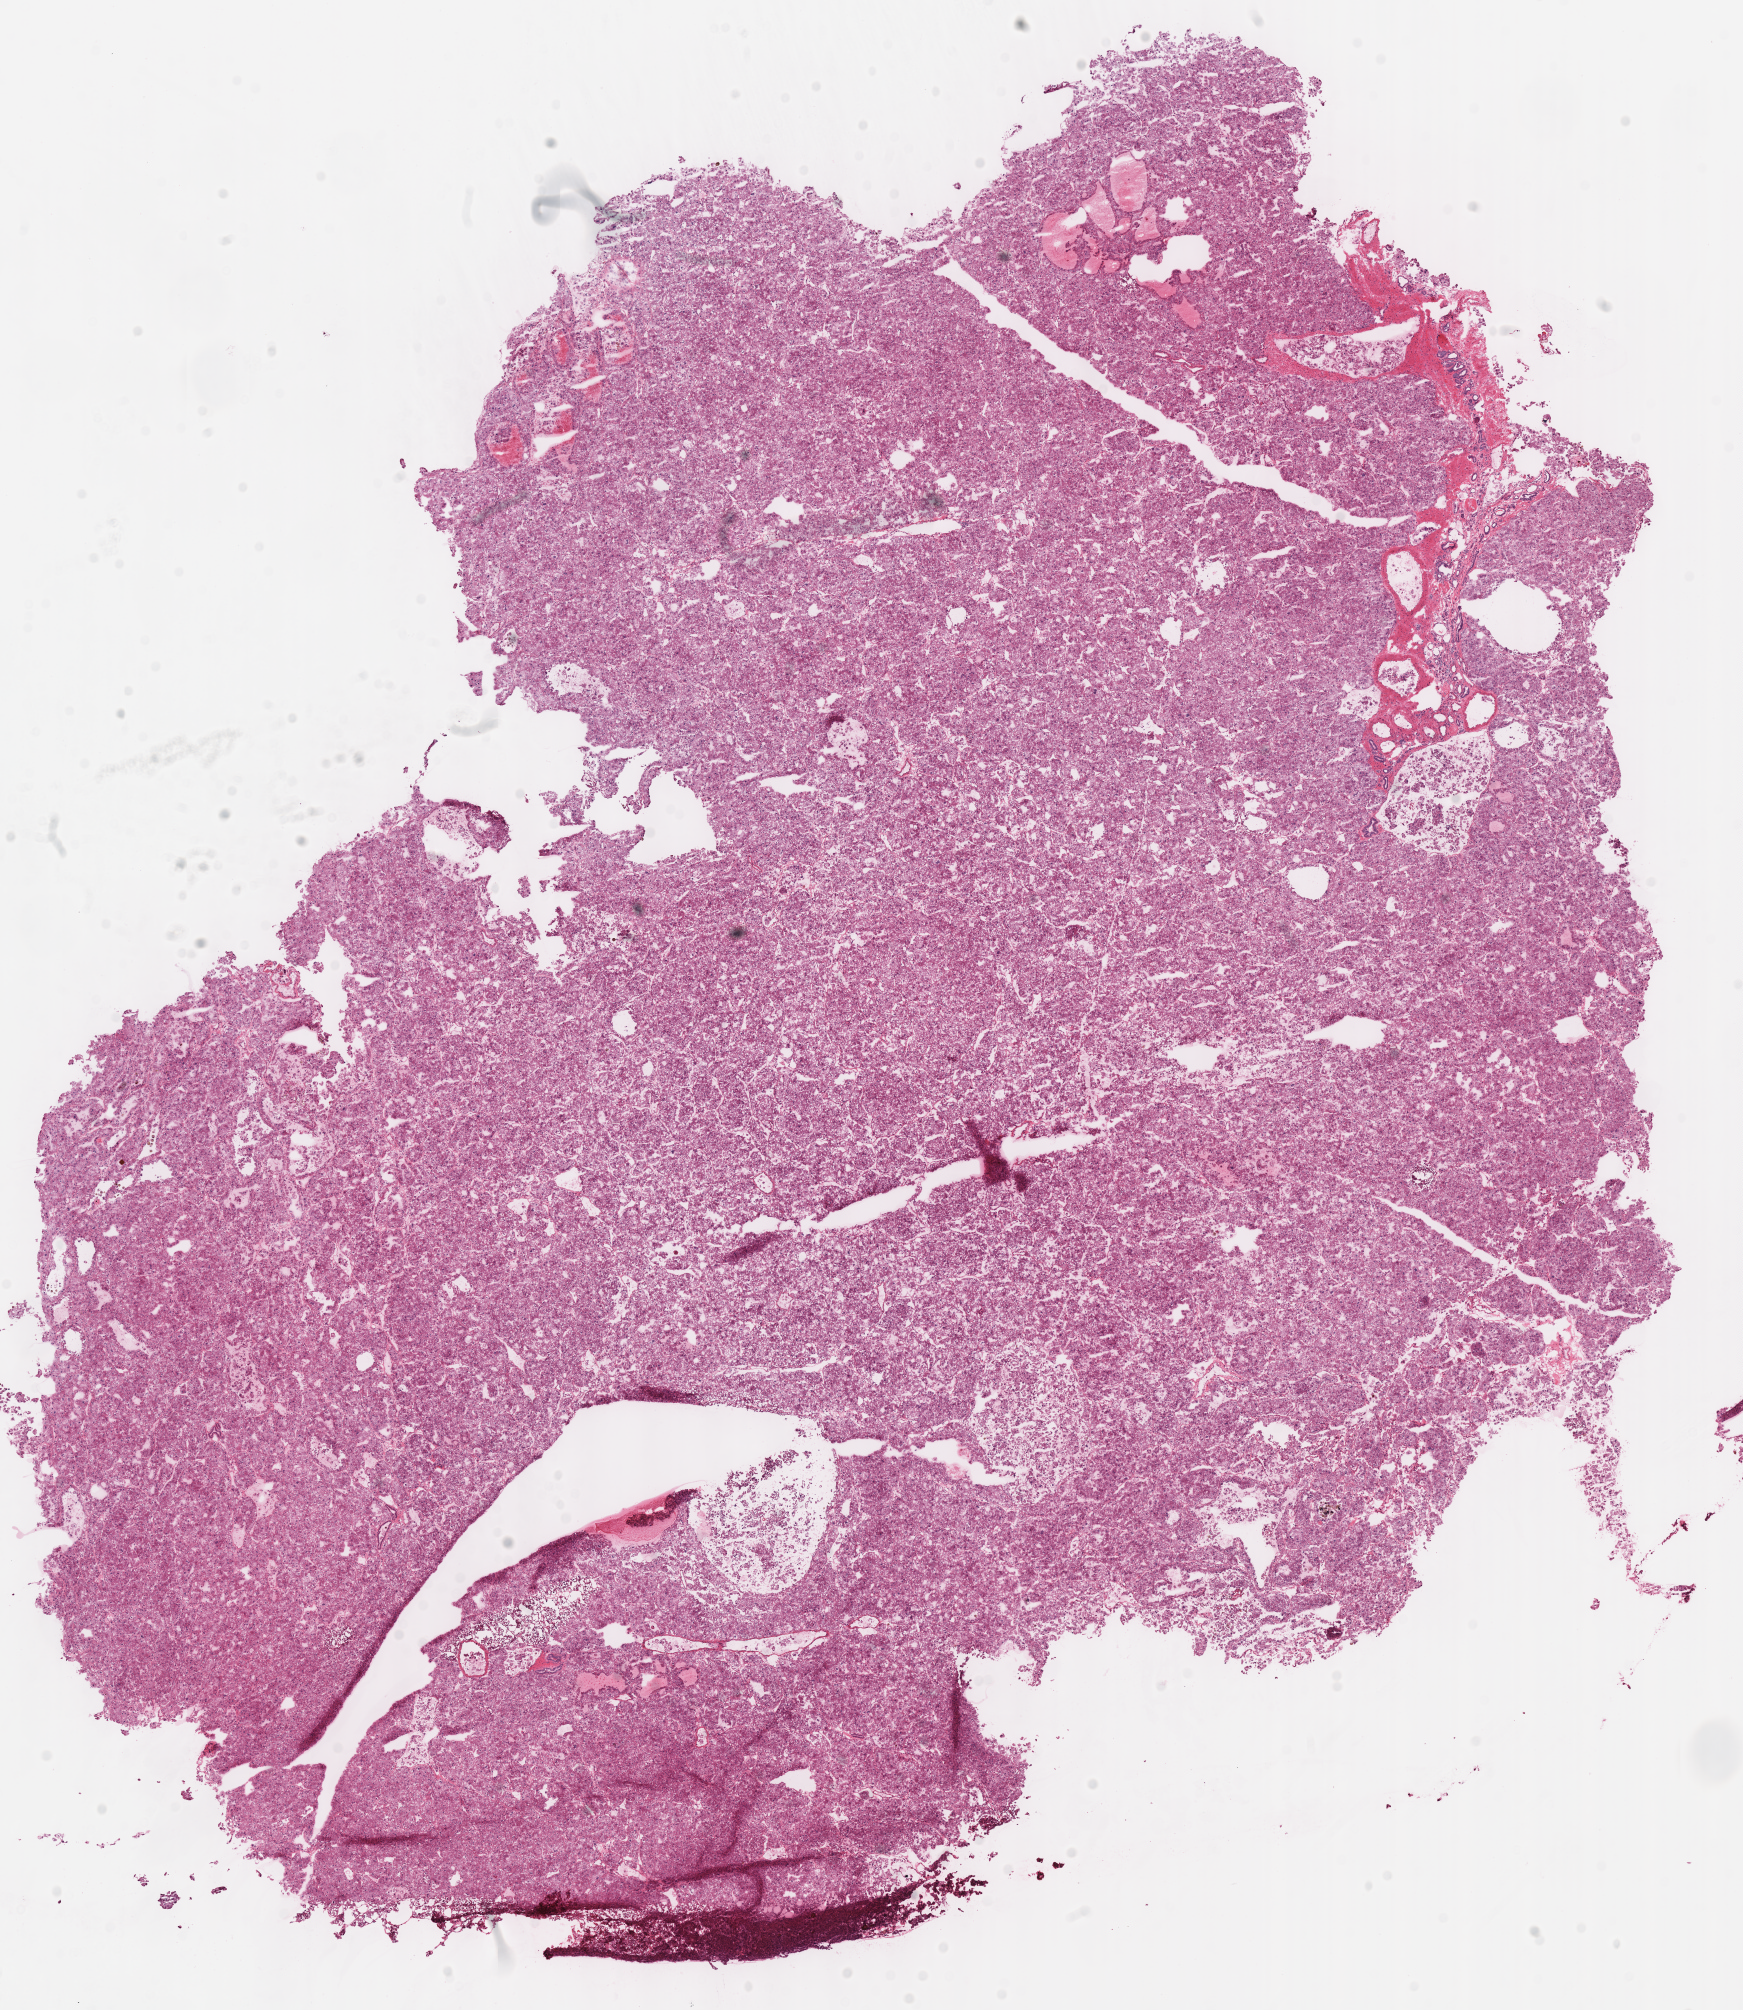
Digitized H&E tissue section (whole slide), a low-resolution overview of the entire scanned area, about 13.7 x 15.8 mm (slide scanned at 40x); frozen section from the top of the tissue portion; sample: primary tumour, kidney. Male patient; age at initial diagnosis 72 years. Composition of this section per pathologist review: tumour cells 95%, tumour nuclei 90%, normal cells 0%, stromal cells 5%, necrosis 0%.
* histologic diagnosis: Renal cell carcinoma, chromophobe type
* AJCC pathologic stage: III (6th edition)
* laterality: right
* TNM: T3 N0 M0
* lymph nodes positive (case pathology): 0 of 6 examined